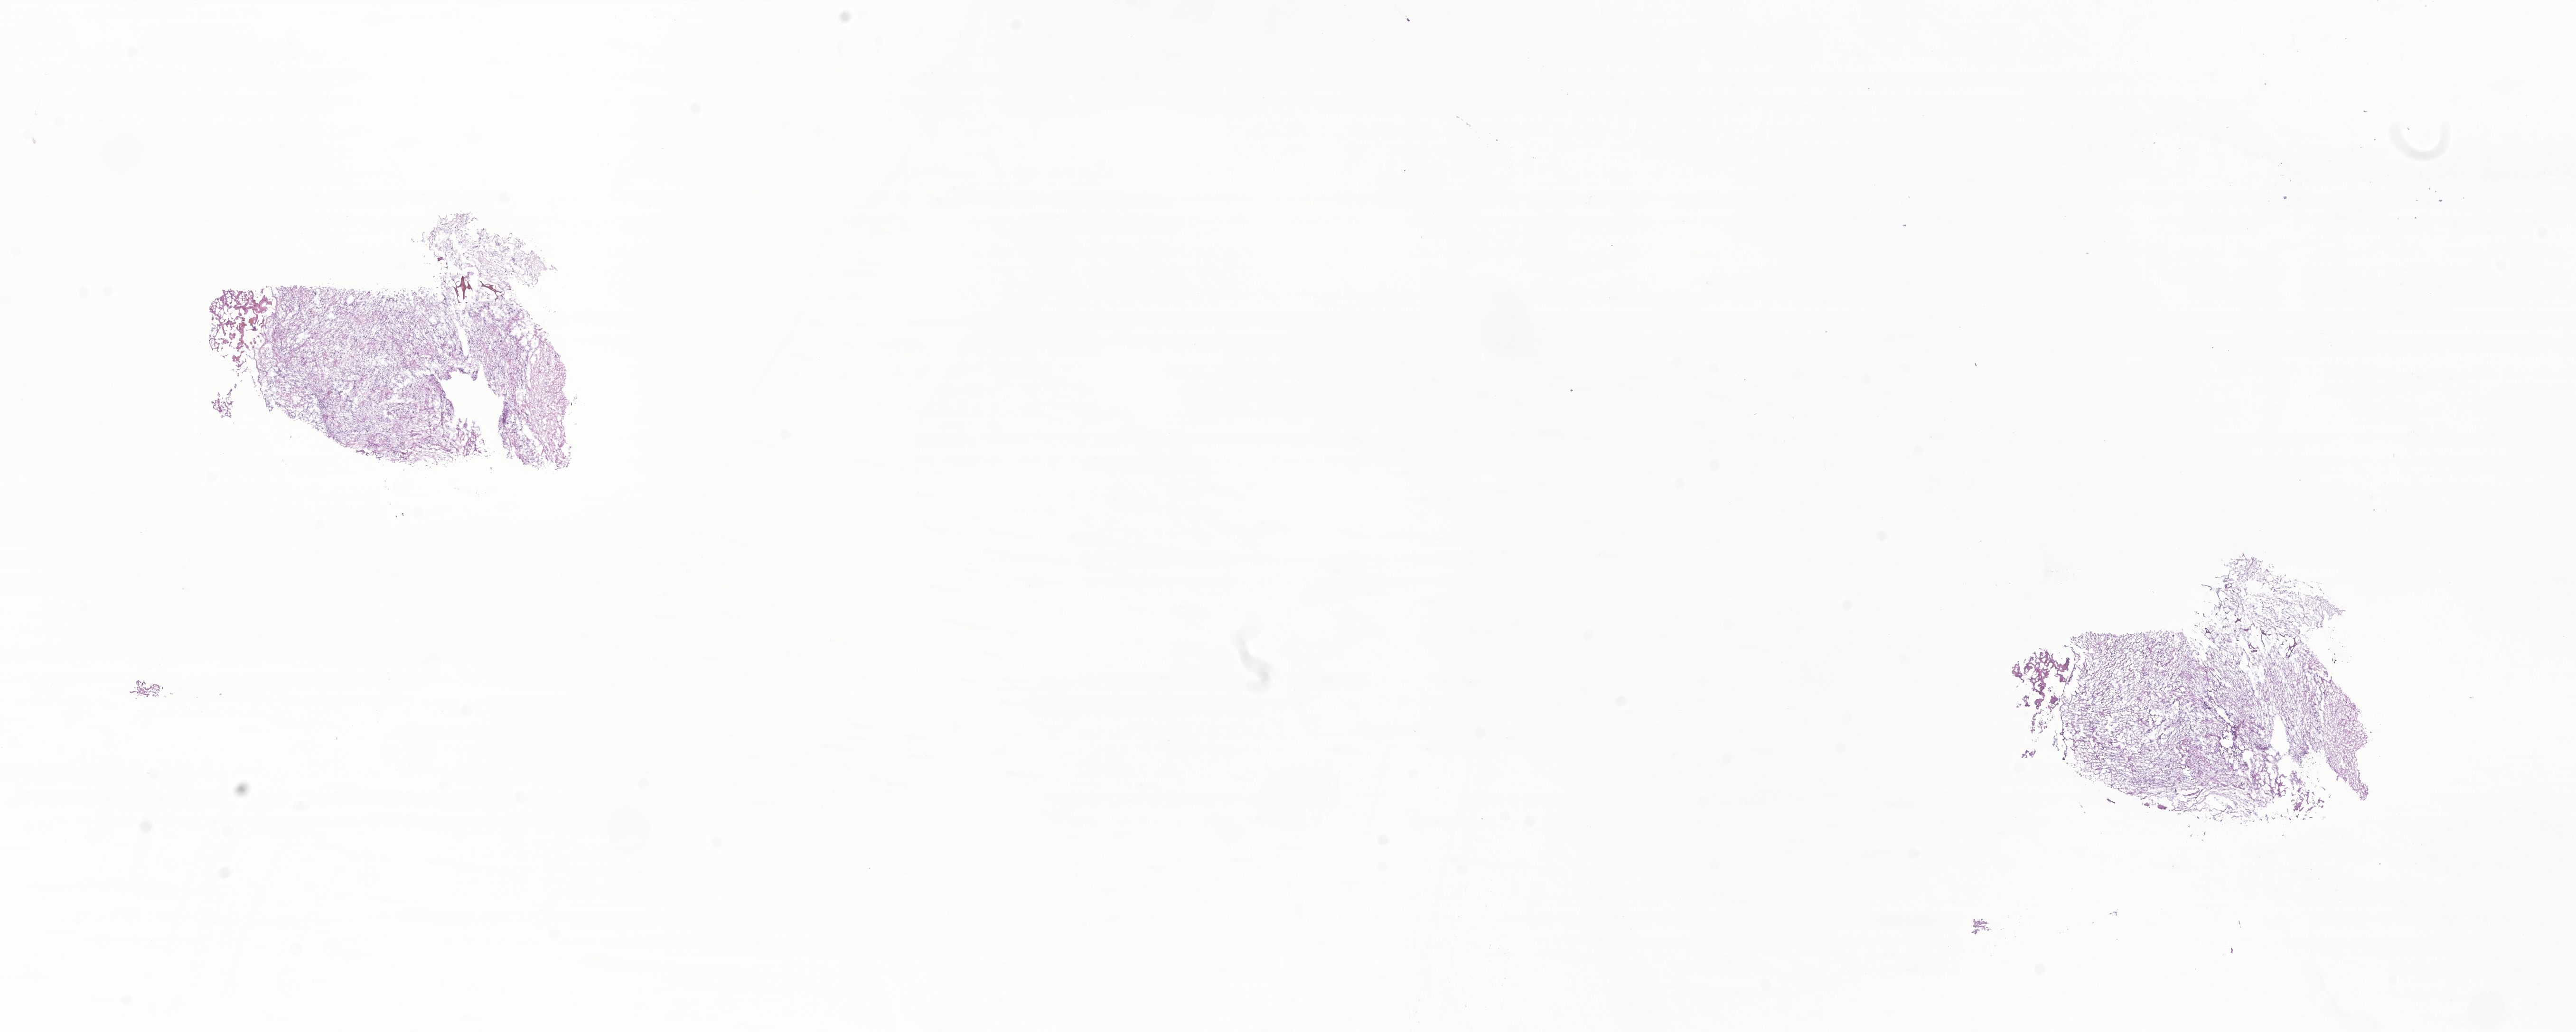
Whole-slide image, H&E stain of tumor tissue from the cerebellum — a low-resolution overview of the entire scanned area, about 22.9 x 9.2 mm; cryosection (OCT / tissue freezing medium). Patient: female, age 62 months (5 years 2 months).
Diagnosis (ICD-O-3 morphology term): Glioma, malignant.